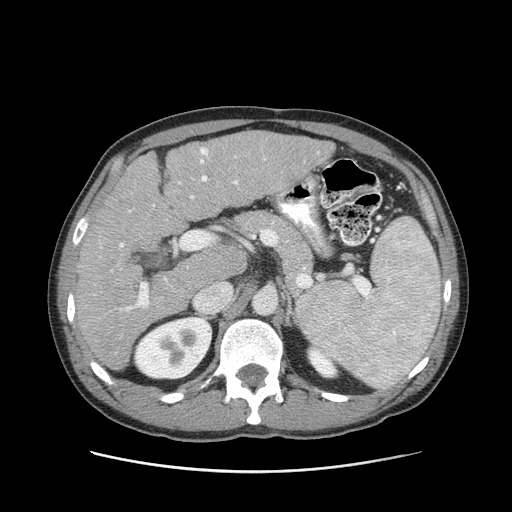
Contrast-enhanced abdominal CT (liver protocol), one axial slice. Position 54 of 93 along the scan axis. 120 kVp. Soft-tissue window (W 400 / L 40 HU). 512 × 512 image matrix, field of view 380 × 380 mm. From the clinical record (not read from this slice): diagnosis: hepatocellular carcinoma (patient treated with transarterial chemoembolisation; whether this scan precedes or follows treatment is not stated here); TNM stage (as recorded): Stage-II; Child-Pugh class: A; tumour nodularity: multinodular; tumour size: 1 cm.
Annotated regions visible in this slice (semi-automatically segmented with operator editing):
- liver parenchyma outside the tumour (the mass and vessels are separate outlines, so this box may not span the whole liver): bounding box [x1, y1, x2, y2] px = [75, 130, 334, 370]
- liver vessels: [111, 147, 319, 312]